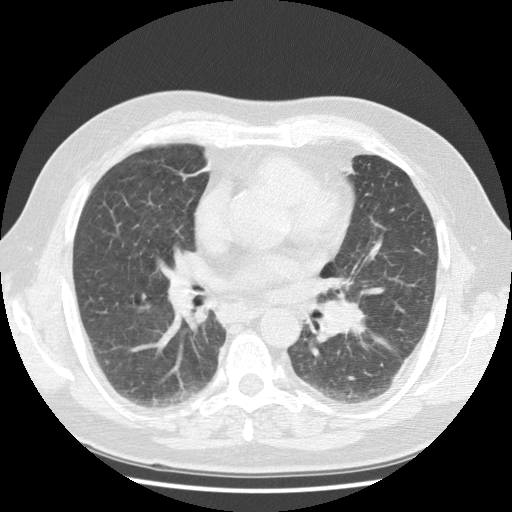
Low-dose screening chest CT, one axial slice. Position 60 of 108 along the scan axis. Reconstruction kernel STANDARD. 120 kVp. Lung window (W 1500 / L -600 HU). 2.5 mm slice thickness. 512 × 512 image matrix.
Structures marked on this image (outlined manually by an expert reader):
- lesion 1 (tumor, hilum of left lung): bounding box (x1, y1, x2, y2) in pixels: (320, 301, 364, 337)